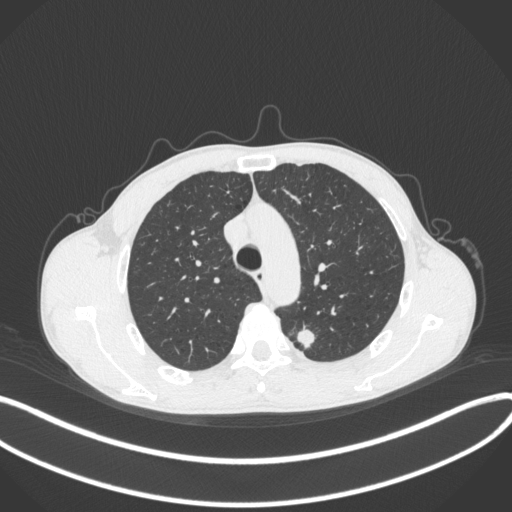
Chest CT, one axial slice. Position 297 of 429 along the scan axis. Reconstruction kernel B31f. 120 kVp. Lung window (W 1500 / L -600 HU). 1 mm slice thickness. 512 × 512 image matrix, field of view 400 × 400 mm. Male patient, age 51 years. Case-level facts recorded for this patient, not image findings: clinical TNM (as recorded): T2a N1 M1.
Outlined on this slice (bounding box drawn by a radiologist):
- lung tumour (recorded histology: adenocarcinoma): bounding box [x1, y1, x2, y2] px = [295, 324, 317, 352]